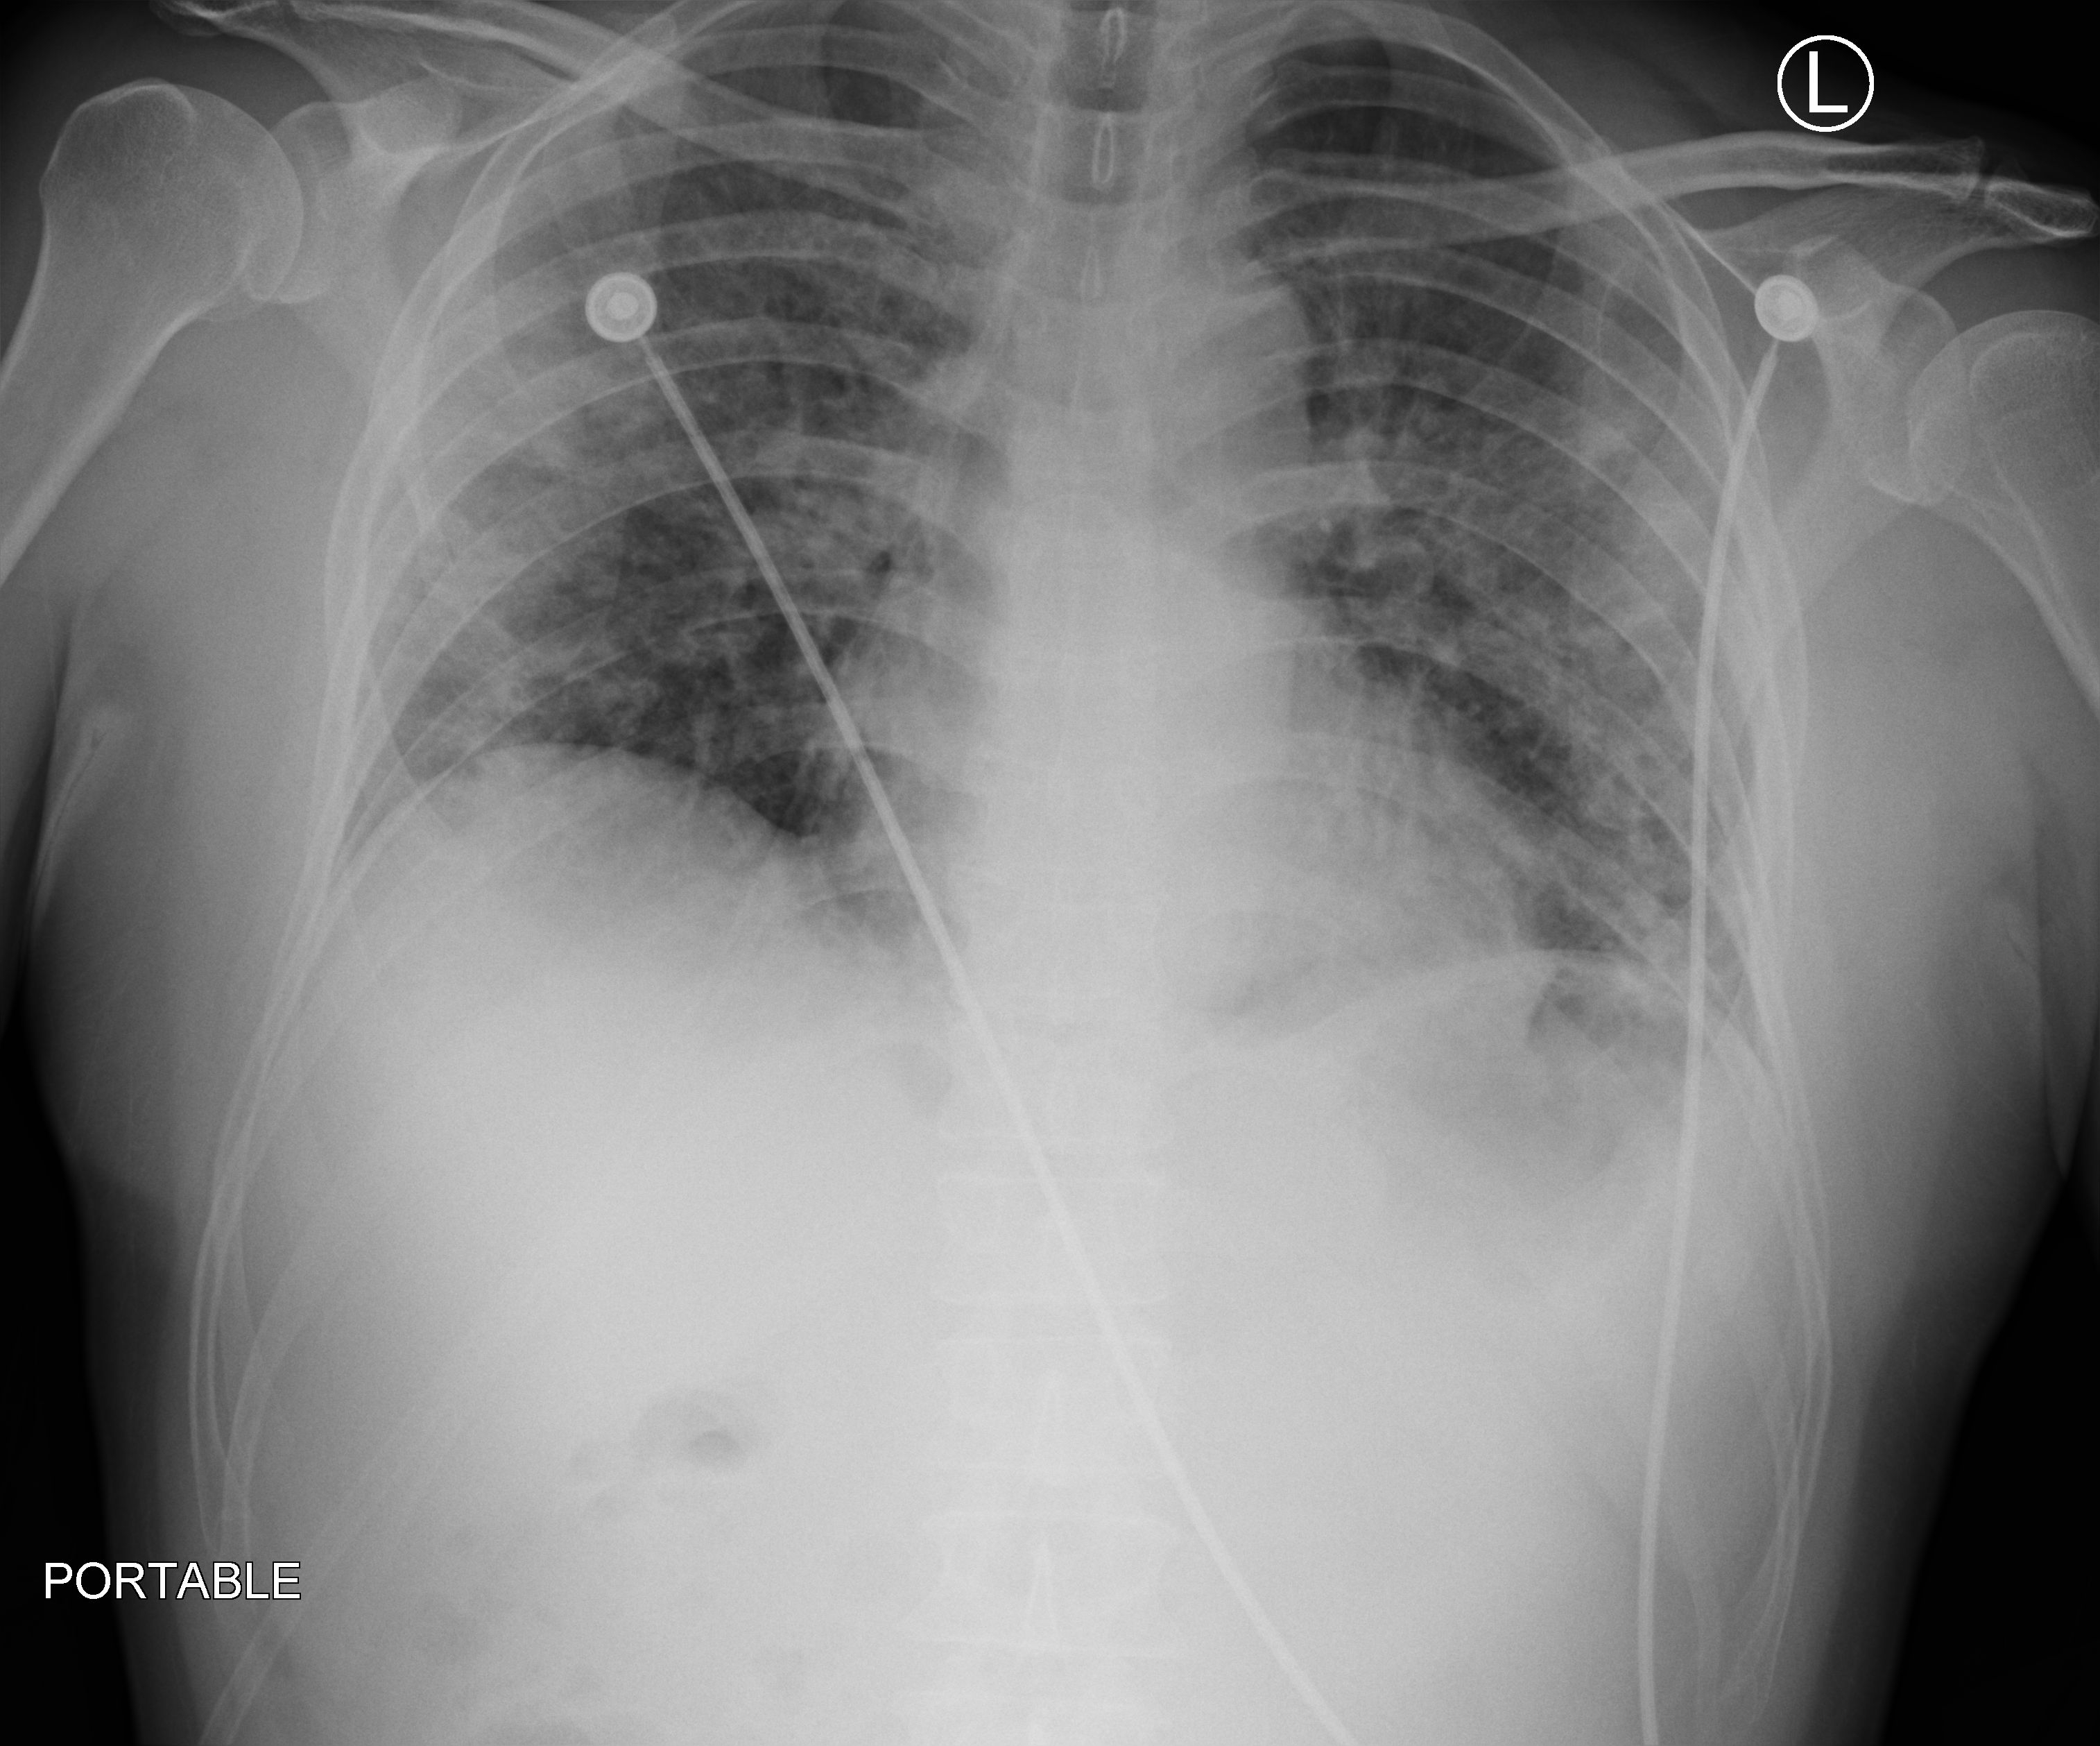
Chest X-ray (portable); anteroposterior (AP) projection. Patient hospitalised with COVID-19; male, aged 18–59 years.
Admission-level facts for this patient (not findings on this image; timing relative to this image not recorded): smoking status (admission record): never; mechanically ventilated during this hospital stay: no; COPD (admission record): no.